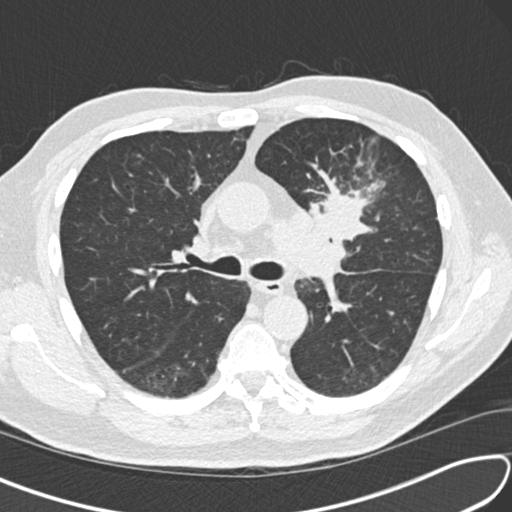
Low-dose screening chest CT, one axial slice; slice 98 of 156 in the series (ordered by position); lung window (W 1500 / L -600 HU); 2 mm slice thickness; 512 × 512 image matrix, field of view 340 × 340 mm.
Annotated regions visible in this slice (manually delineated by an expert):
- lesion 1 (tumor, upper lobe of left lung): bounding box (x1, y1, x2, y2) in pixels: (321, 191, 365, 242)